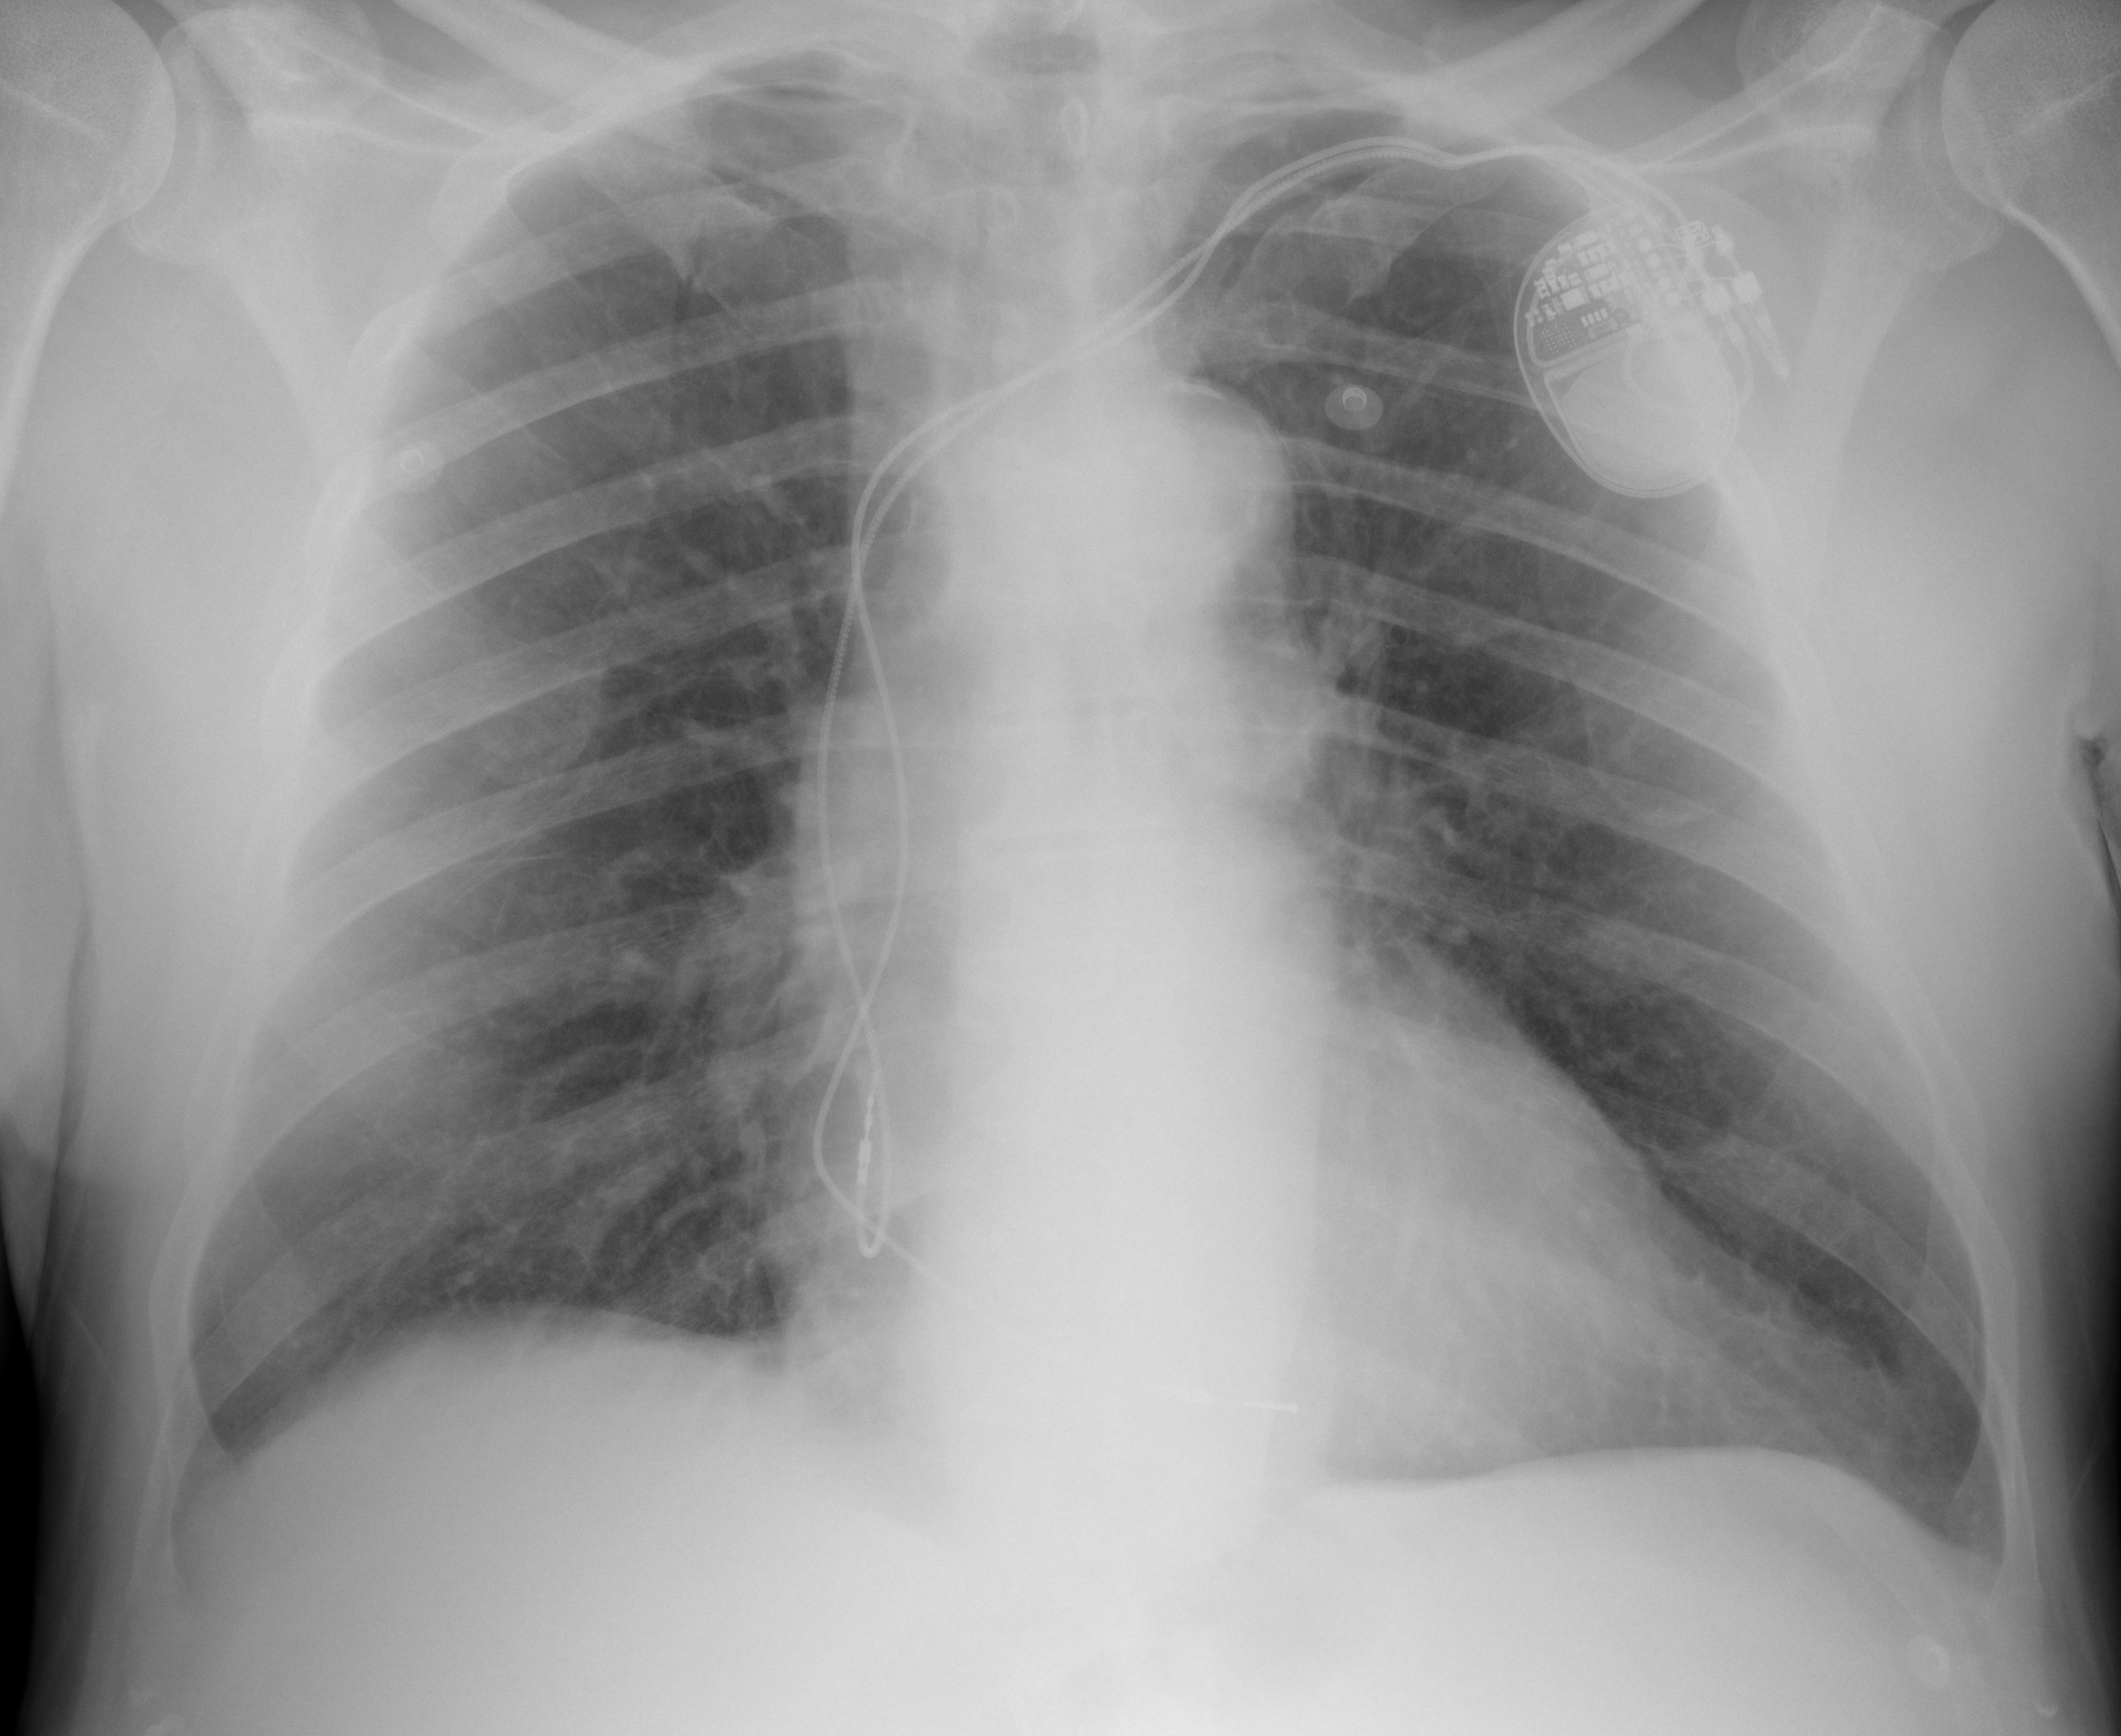
Portable chest radiograph, AP projection. Male patient, age 79 years; imaged 0 days after the COVID-19 diagnosis.
Radiologist's key findings for this exam: No significant airspace consolidation evident bilaterally.